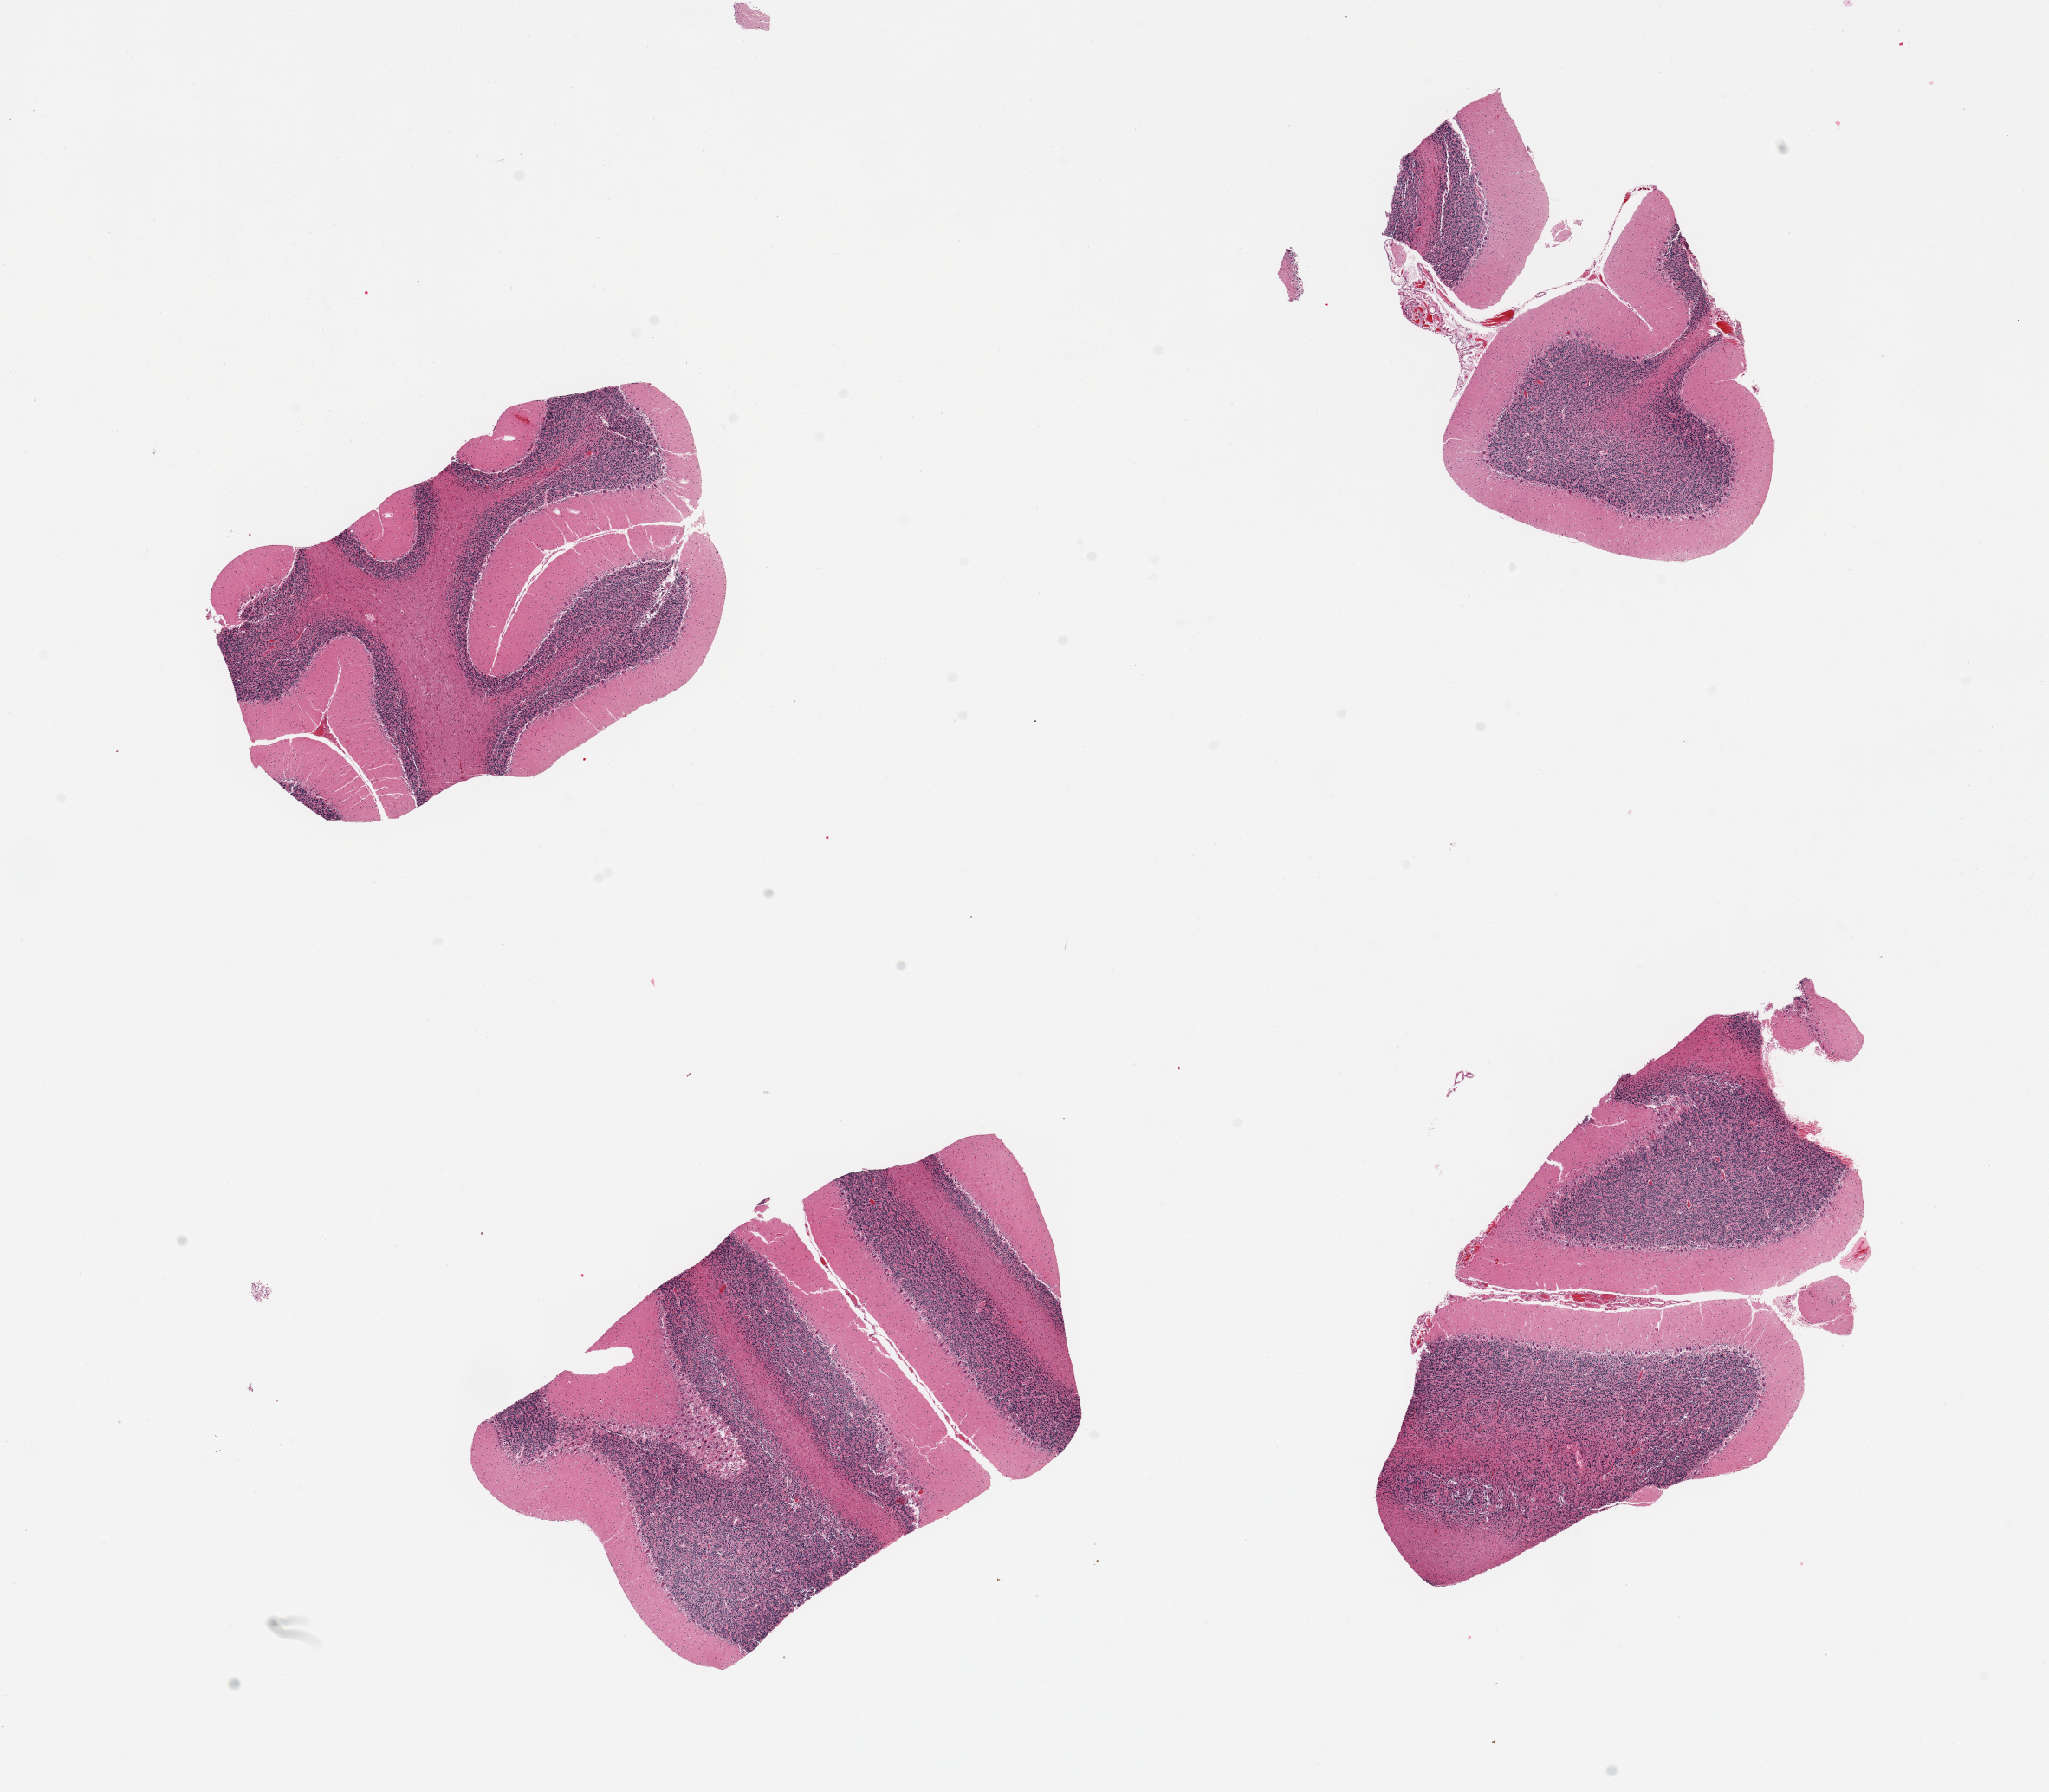
Digitized haematoxylin and eosin-stained section — shown as a low-resolution overview of the whole scanned area (about 18.7 x 16.4 mm). PAXgene-fixed, paraffin-embedded tissue. Target tissue: cerebellum. Tissue donor sample. Female donor.
Reviewer comment on this tissue sample: 4 pieces, no abnormalities.